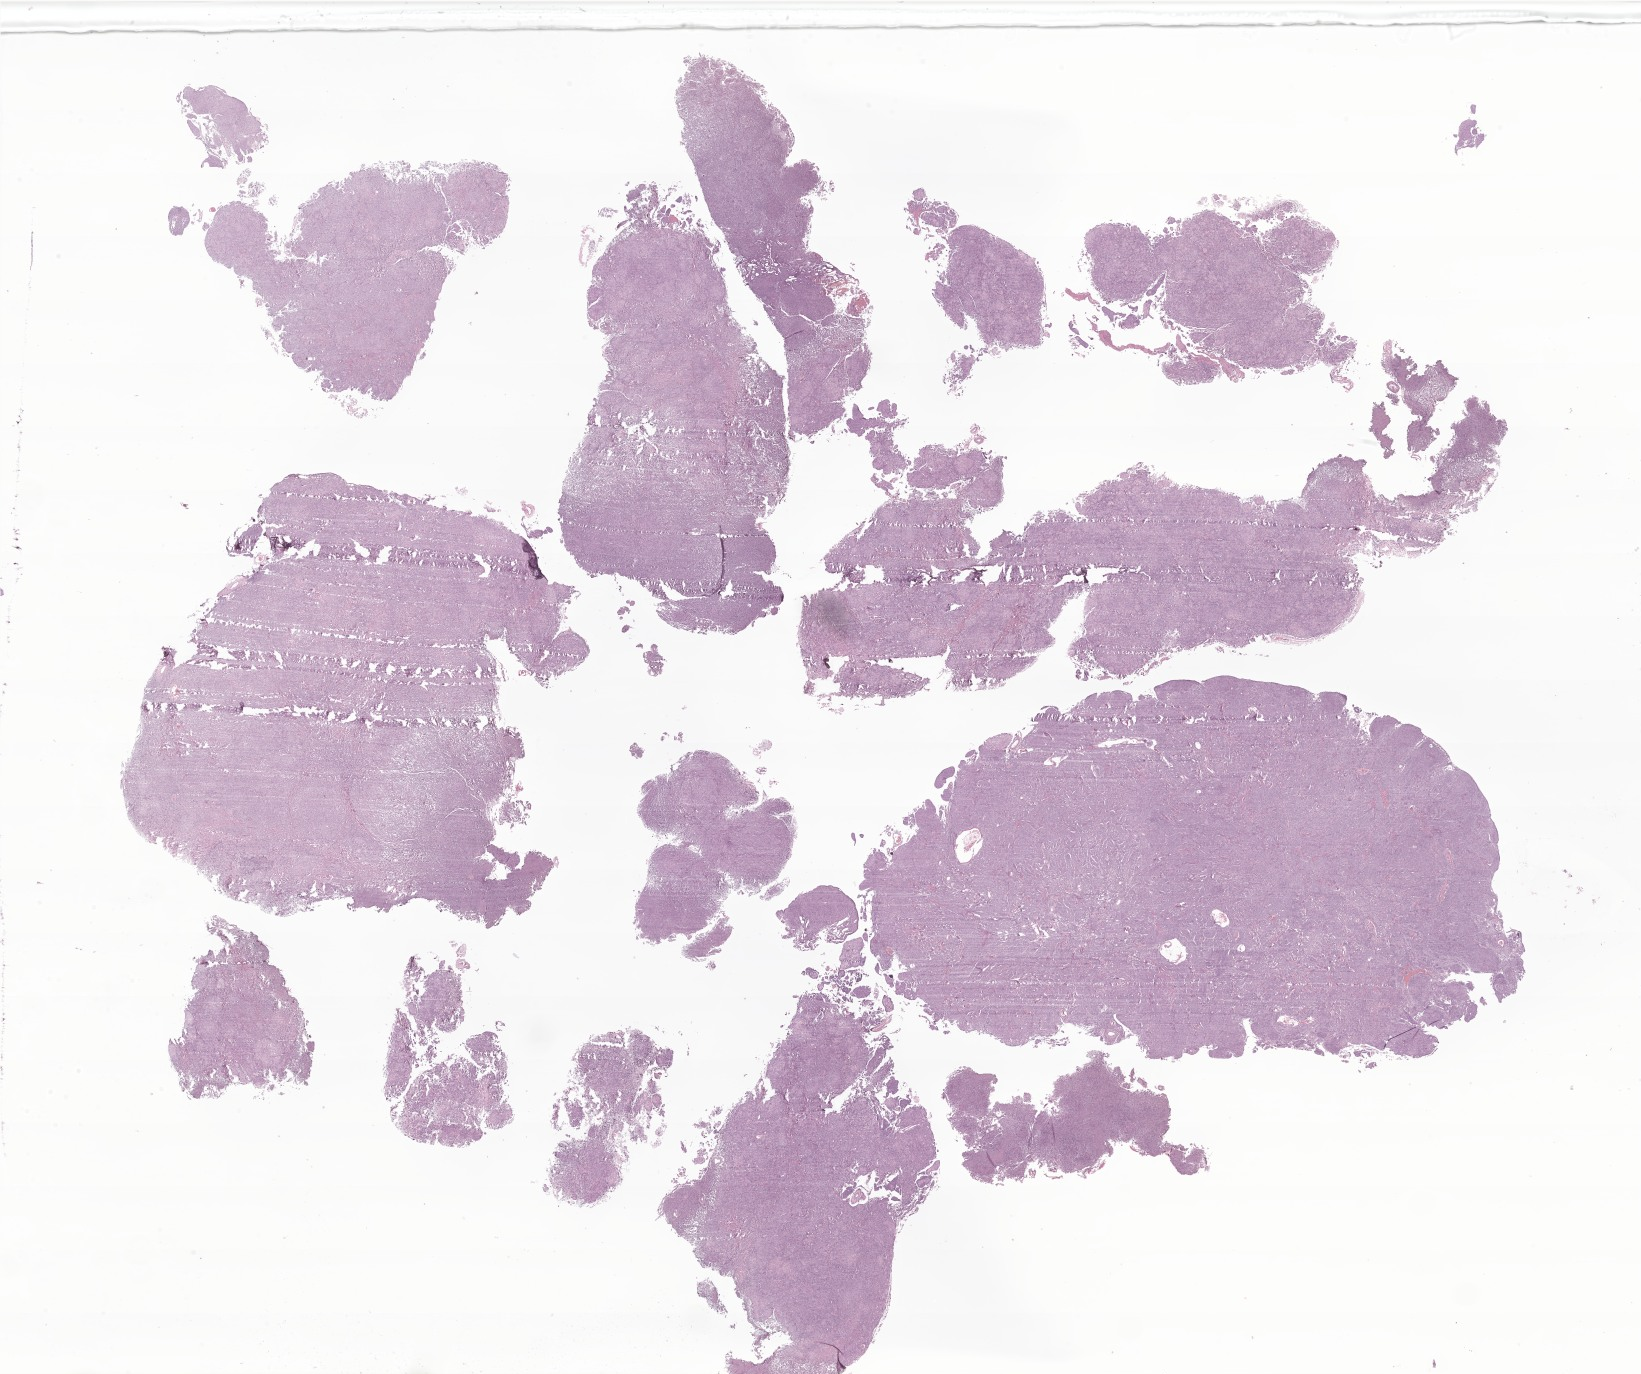
Whole-slide image, hematoxylin and eosin (H&E) stain of tumor tissue from the brain, shown as a low-resolution overview of the whole scanned area (about 27.7 x 23.2 mm), formalin-fixed paraffin-embedded section. Patient male; age 103 months.
Diagnosis: Transitional meningioma.